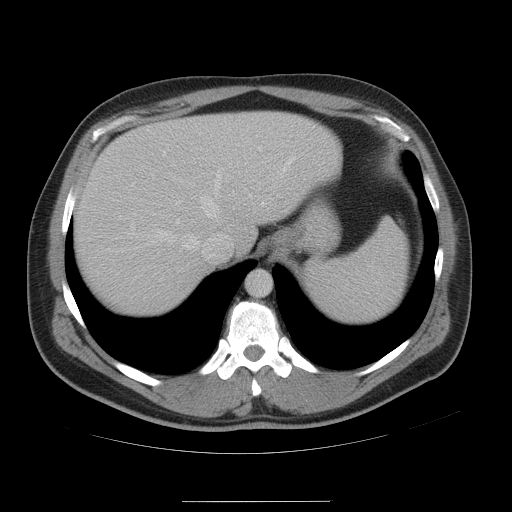
Contrast-enhanced abdominal CT, one axial slice; slice 41 of 54 in the series (ordered by position); soft-tissue window (W 400 / L 40 HU); 5 mm slice thickness; 512 × 512 image matrix, field of view 436 × 436 mm. Male patient, age 40 years. Case-level facts recorded for this patient, not image findings: diagnosis: colorectal cancer liver metastases, imaged before liver resection; multiple liver metastases: no; largest metastasis: 15 cm; disease in both lobes: no.
Structures marked on this image (outlined manually by an expert reader):
- hepatic veins: bounding box <119,158,295,254> (left, top, right, bottom; pixels)
- liver: <74,111,342,318>
- planned liver remnant (the part of the liver to remain after resection): <170,112,342,272>
- portal vein (with intrahepatic branches): <163,135,244,157>